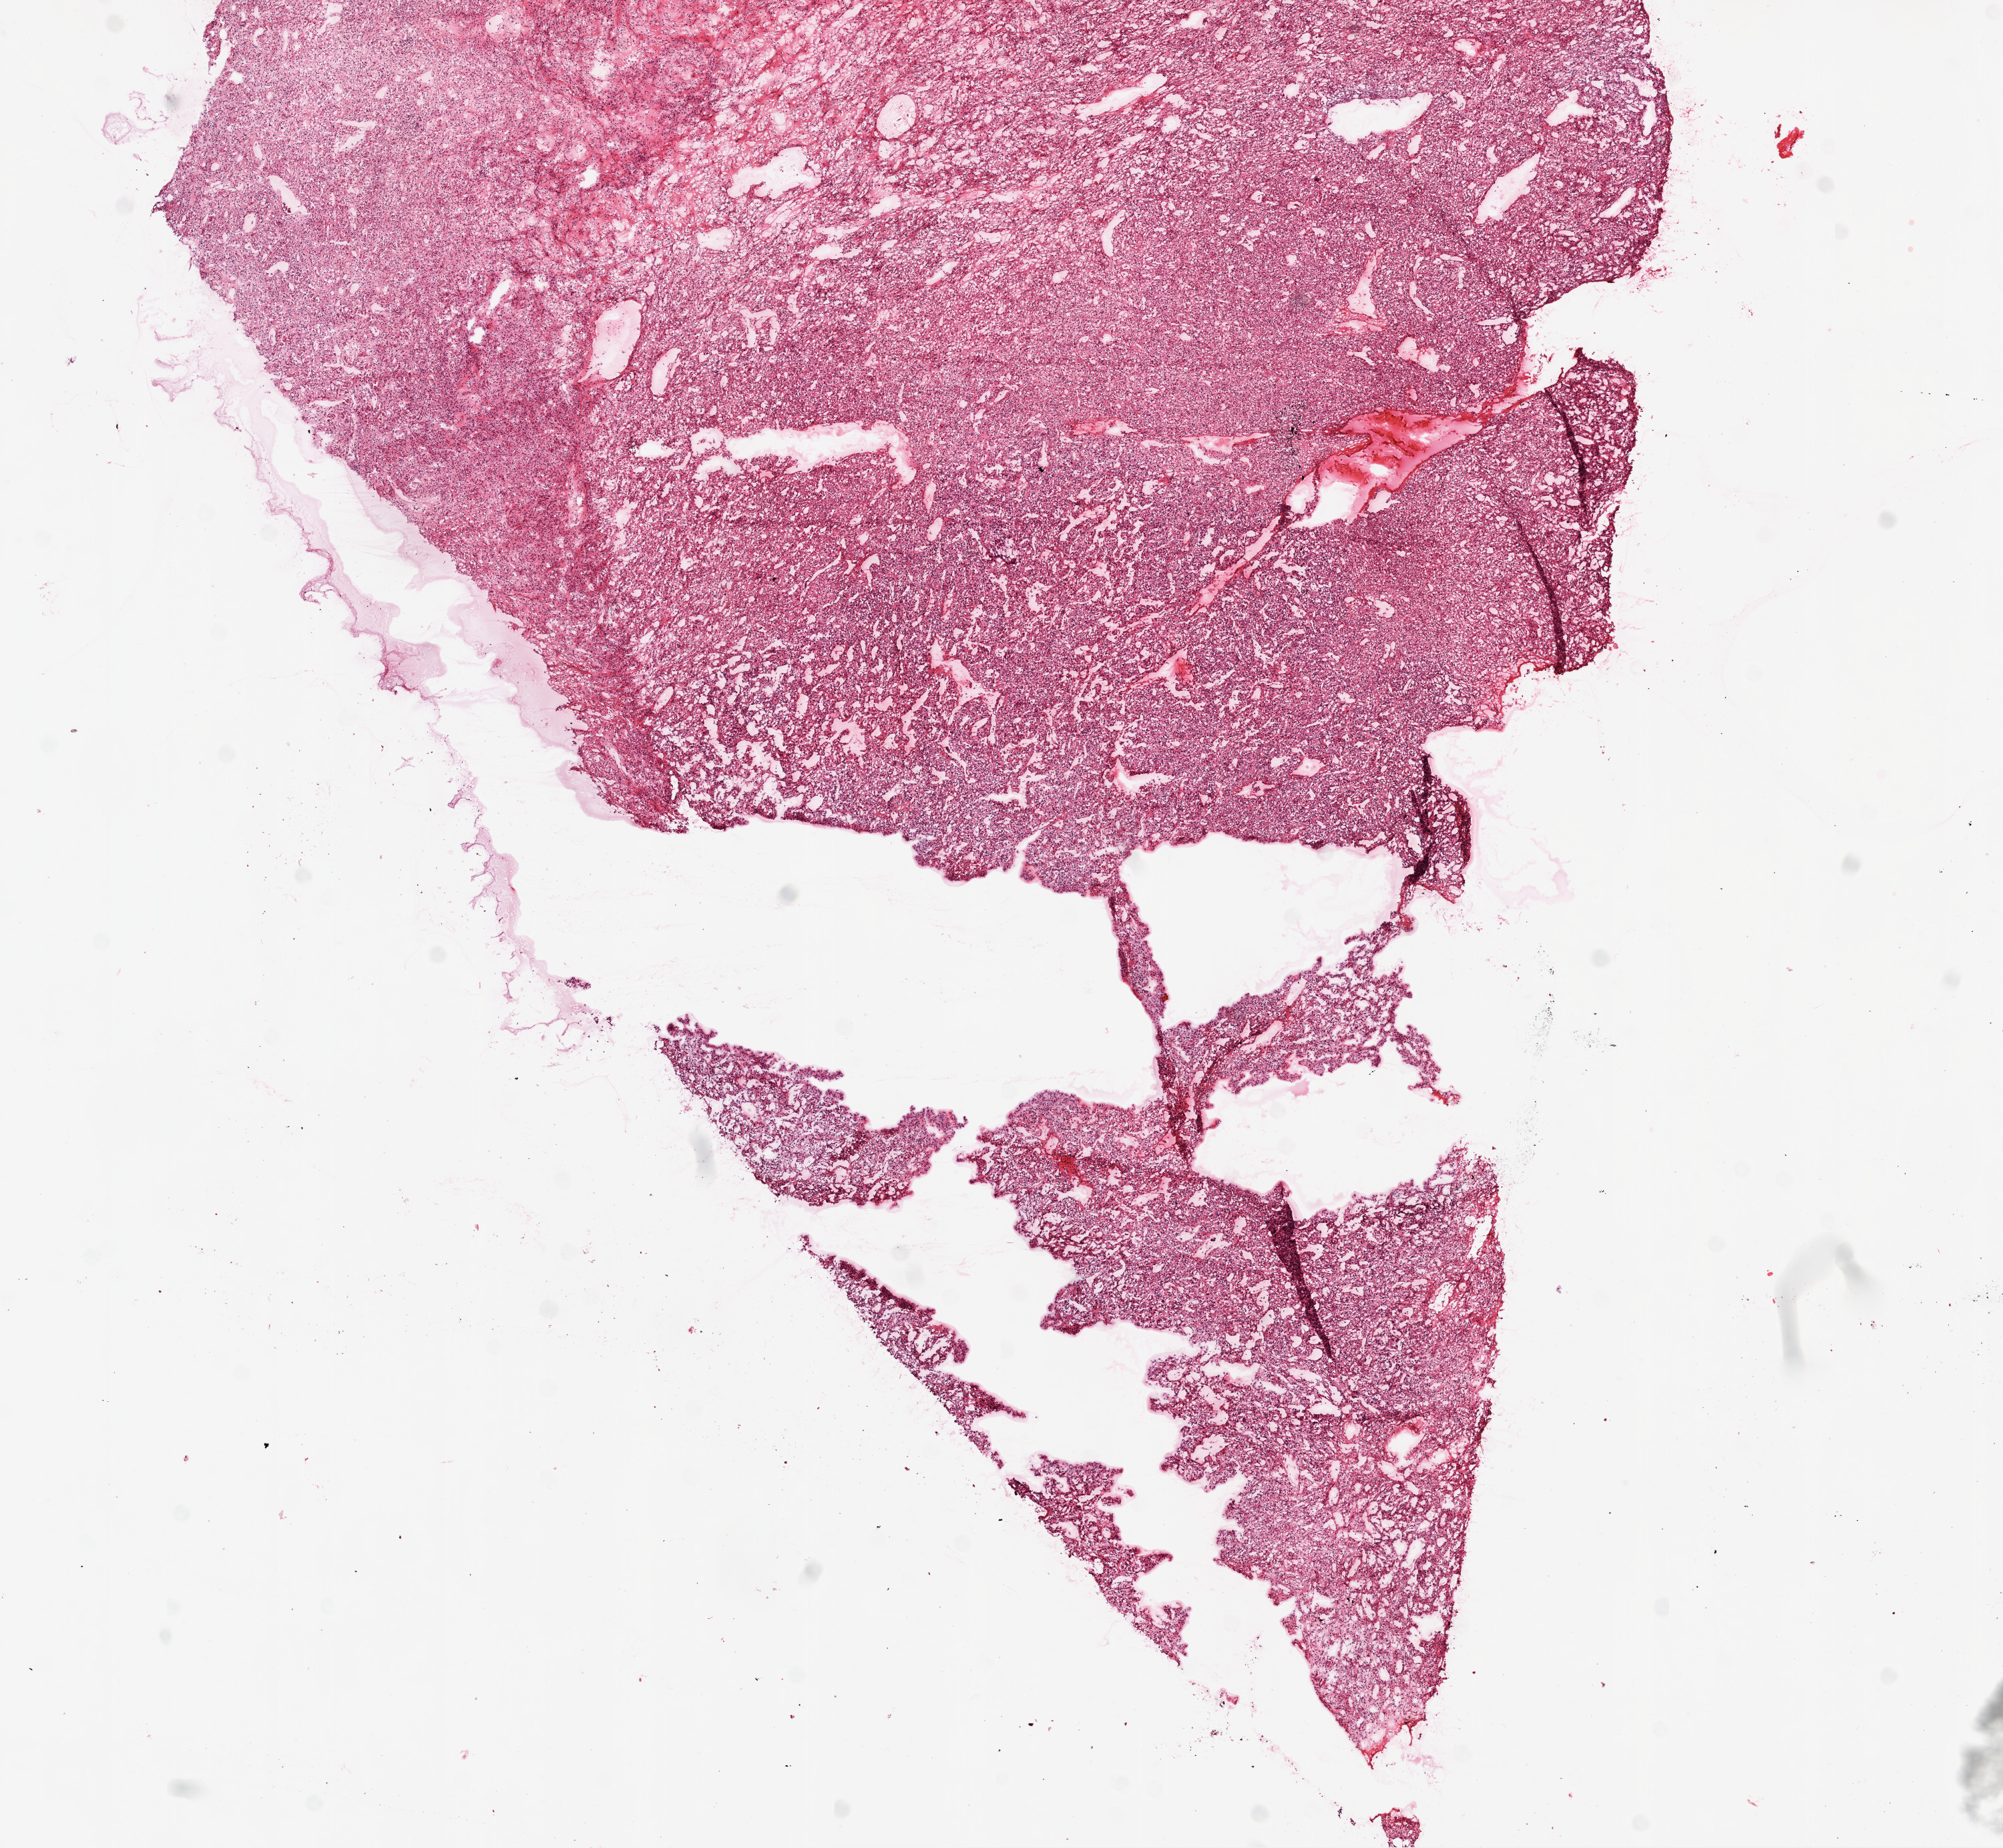
Hematoxylin and eosin (H&E) stained whole-slide image, whole scanned area (about 12.0 x 11.1 mm) shown as a low-resolution overview, frozen section from the top of the tissue portion, sample: primary tumour, kidney. Male patient; age at initial diagnosis 79 years. Histologic grade: G3 (poorly differentiated). Slide review estimates, as recorded: tumour cells 95%, tumour nuclei 90%, normal cells 0%, stromal cells 5%, necrosis 0%.
Histologic diagnosis: Clear cell adenocarcinoma, NOS. AJCC pathologic stage: IV. Laterality: left.